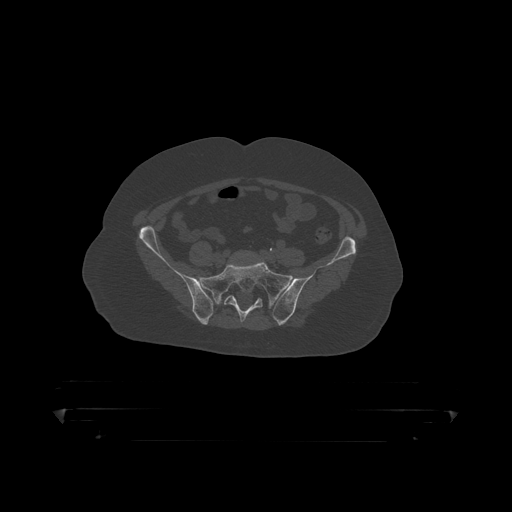
CT including the spine, one axial slice; position 17 of 390 along the scan axis; reconstruction kernel STANDARD; bone window (W 1800 / L 400 HU); 512 × 512 image matrix. Patient: male, 60 years. From the clinical record (not read from this slice): primary cancer: prostate.
Structures marked on this image (semi-automatically segmented with operator editing):
- L5 vertebra: bounding box [x1, y1, x2, y2] px = [247, 251, 250, 254]